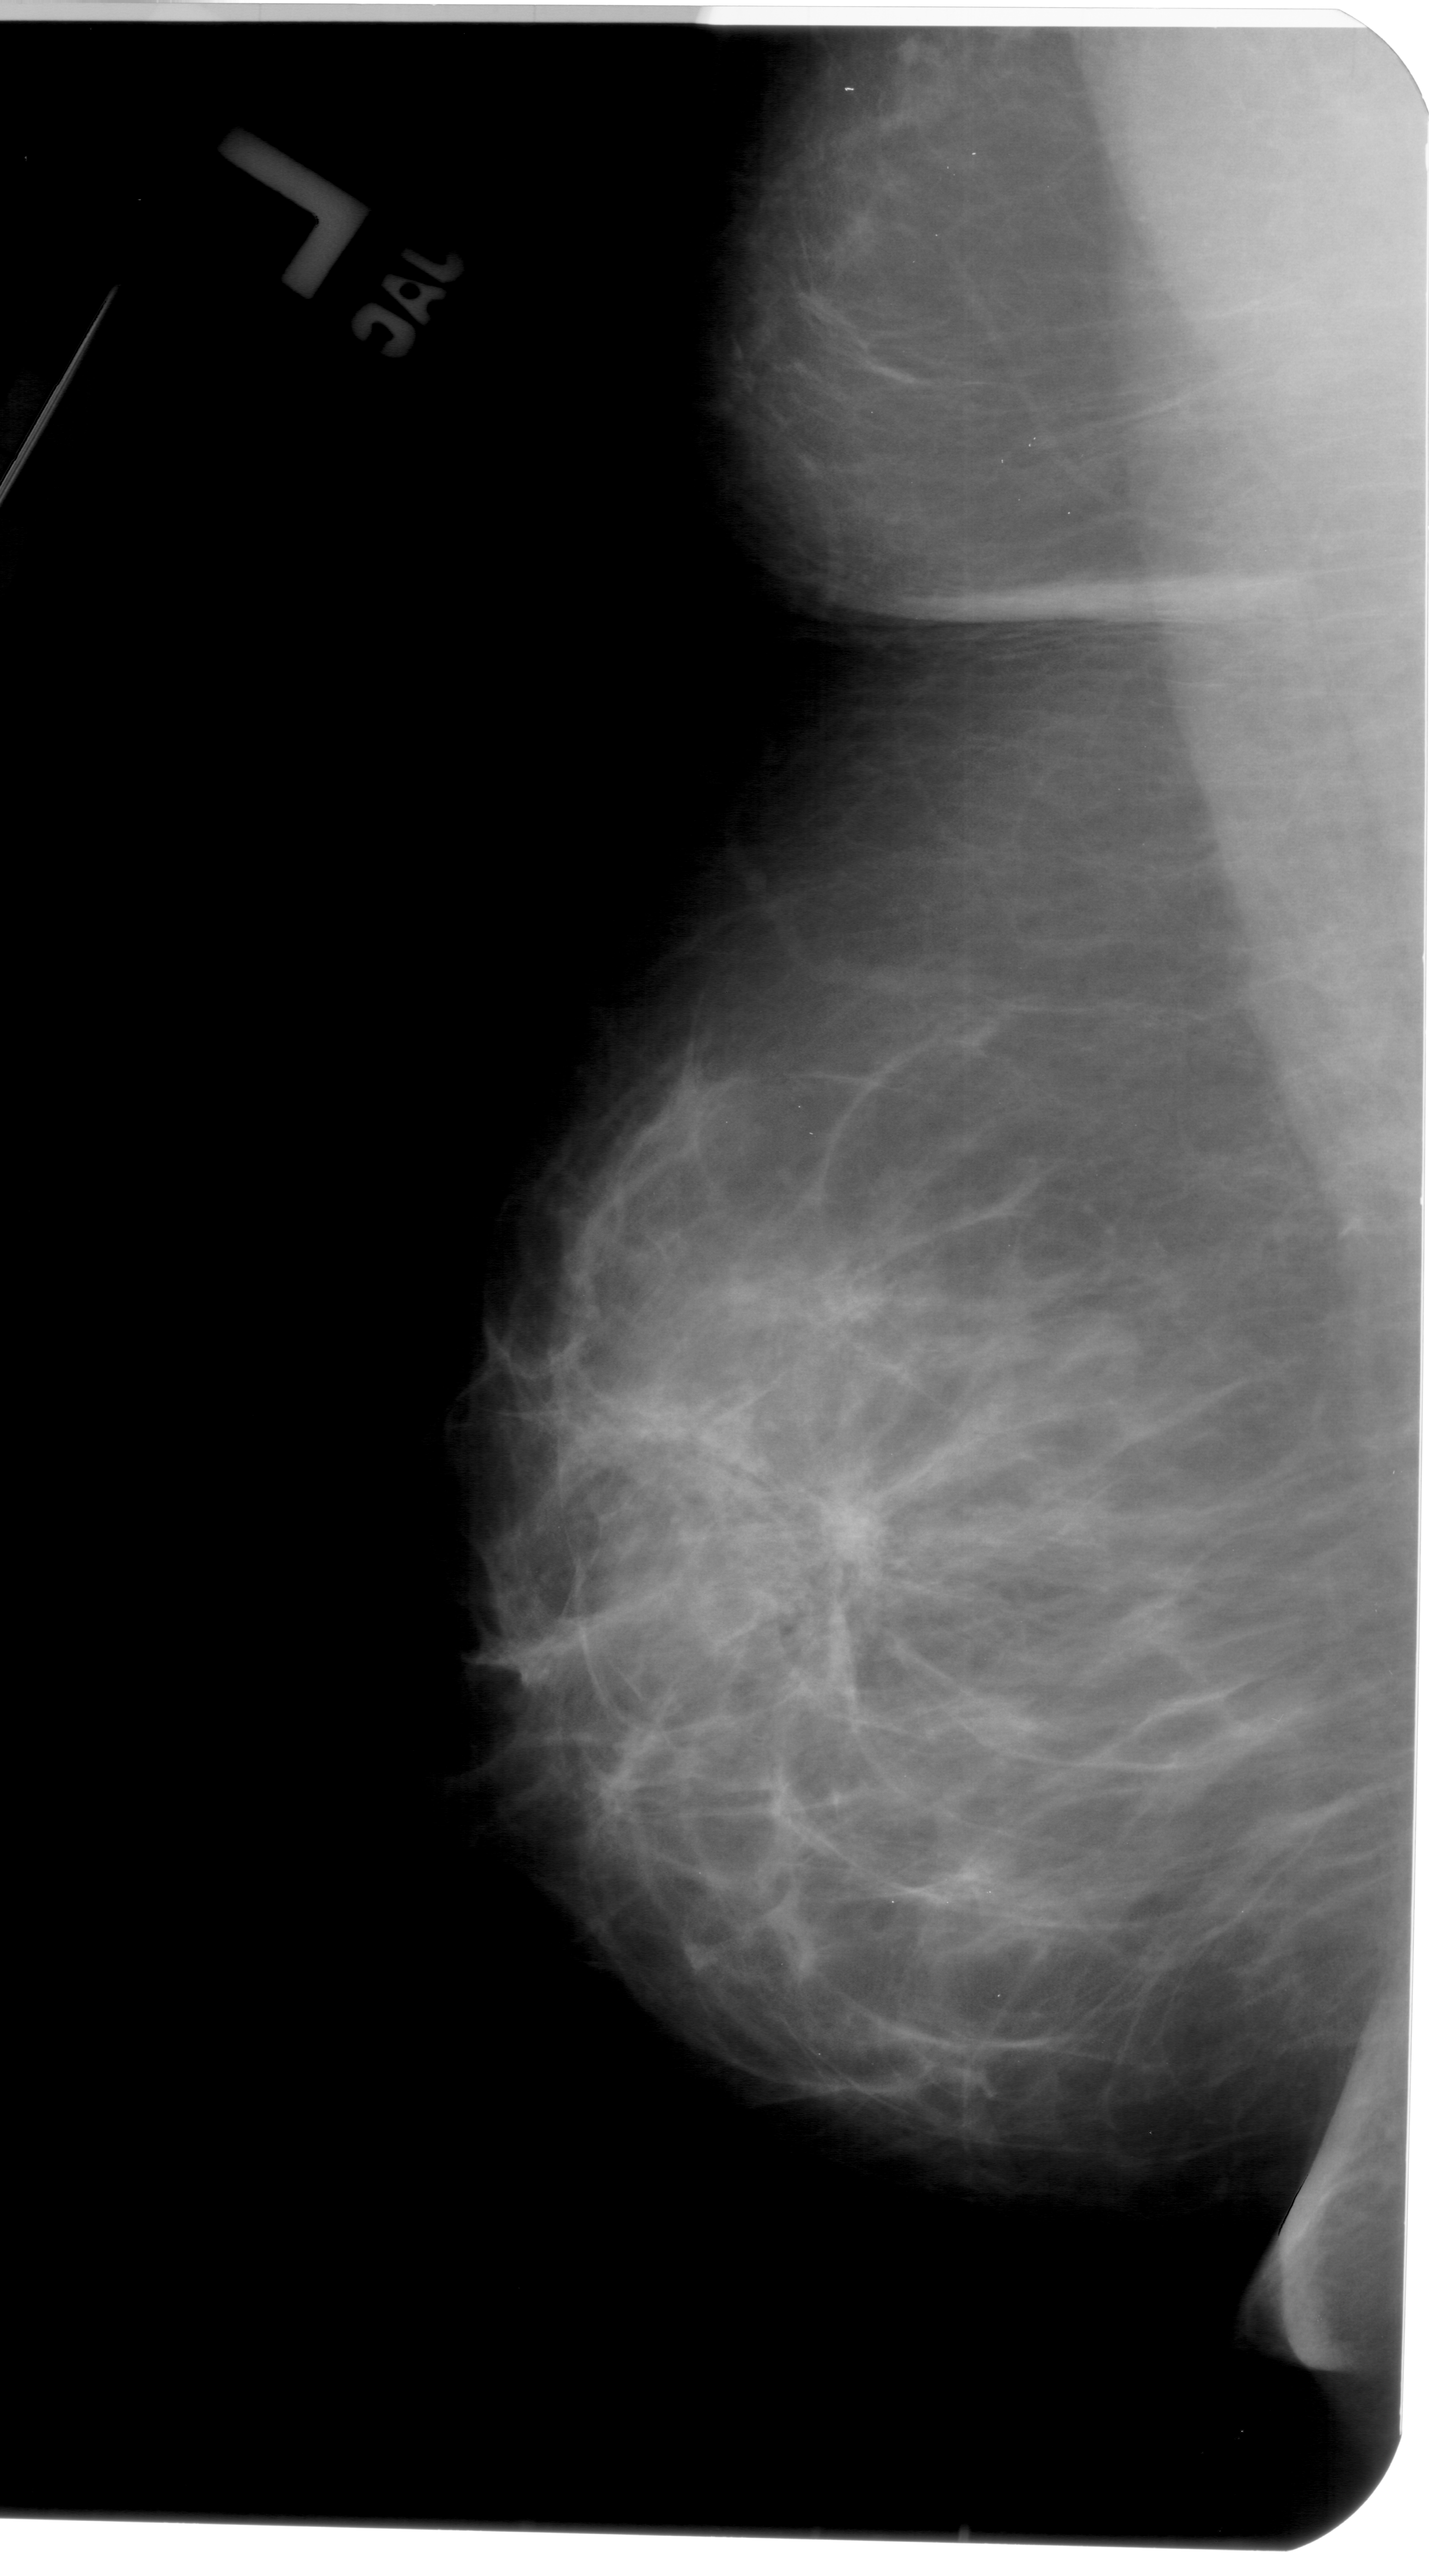
Mammogram (digitized film), left breast, mediolateral oblique (MLO) view, BI-RADS breast density category 3 (scale 1–4).
Radiologist-marked abnormalities on this image: mass, shape architectural distortion, margins ill defined; BI-RADS assessment category 4; pathology (as recorded): benign.